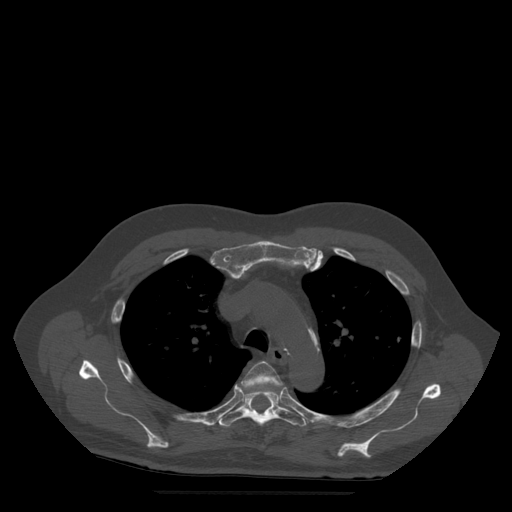
CT including the spine, one axial slice. Slice 380 of 522 in the series (ordered by position). Bone window (W 1800 / L 400 HU). 1.25 mm slice thickness. 512 × 512 image matrix, field of view 420 × 420 mm. Patient age 72 years. From the clinical record (not read from this slice): primary cancer: prostate.
Annotated regions visible in this slice (semi-automatically segmented with operator editing):
- T4 vertebra: box from (x=241, y=361) to (x=283, y=397) px
- T5 vertebra: (x=219, y=389)–(x=308, y=427)